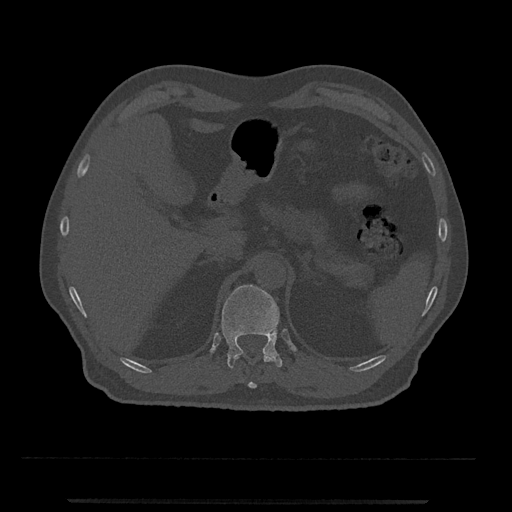
CT including the spine, one axial slice; slice 425 of 797 in the series (ordered by position); reconstruction kernel Br40s/3; bone window (W 1800 / L 400 HU); 0.5 mm slice thickness; 512 × 512 image matrix, field of view 419 × 419 mm. Patient: male, 63 years. Case-level facts recorded for this patient, not image findings: primary cancer: prostate.
Annotated regions visible in this slice (semi-automatic segmentation, software-assisted and operator-edited):
- T11 vertebra: bounding box (x1, y1, x2, y2) in pixels: (235, 351, 273, 388)
- T12 vertebra: (221, 284, 283, 368)